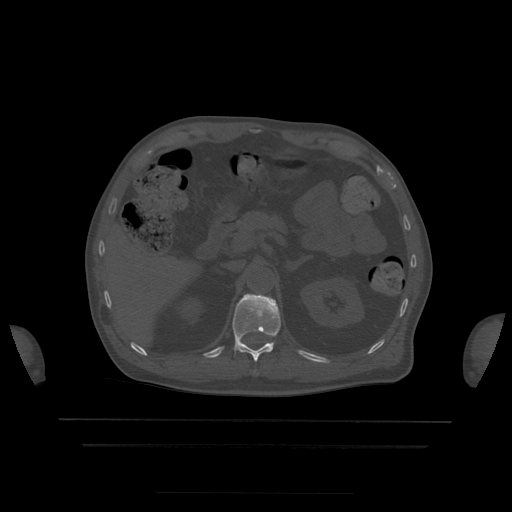
CT including the spine, one axial slice. Slice 193 of 522 in the series (ordered by position). Bone window (W 1800 / L 400 HU). 512 × 512 image matrix, field of view 436 × 436 mm. Patient age 68 years. From the clinical record (not read from this slice): primary cancer: urothelial.
Outlined on this slice (semi-automatic segmentation, software-assisted and operator-edited):
- T12 vertebra: bounding box [x1, y1, x2, y2] px = [233, 294, 281, 362]